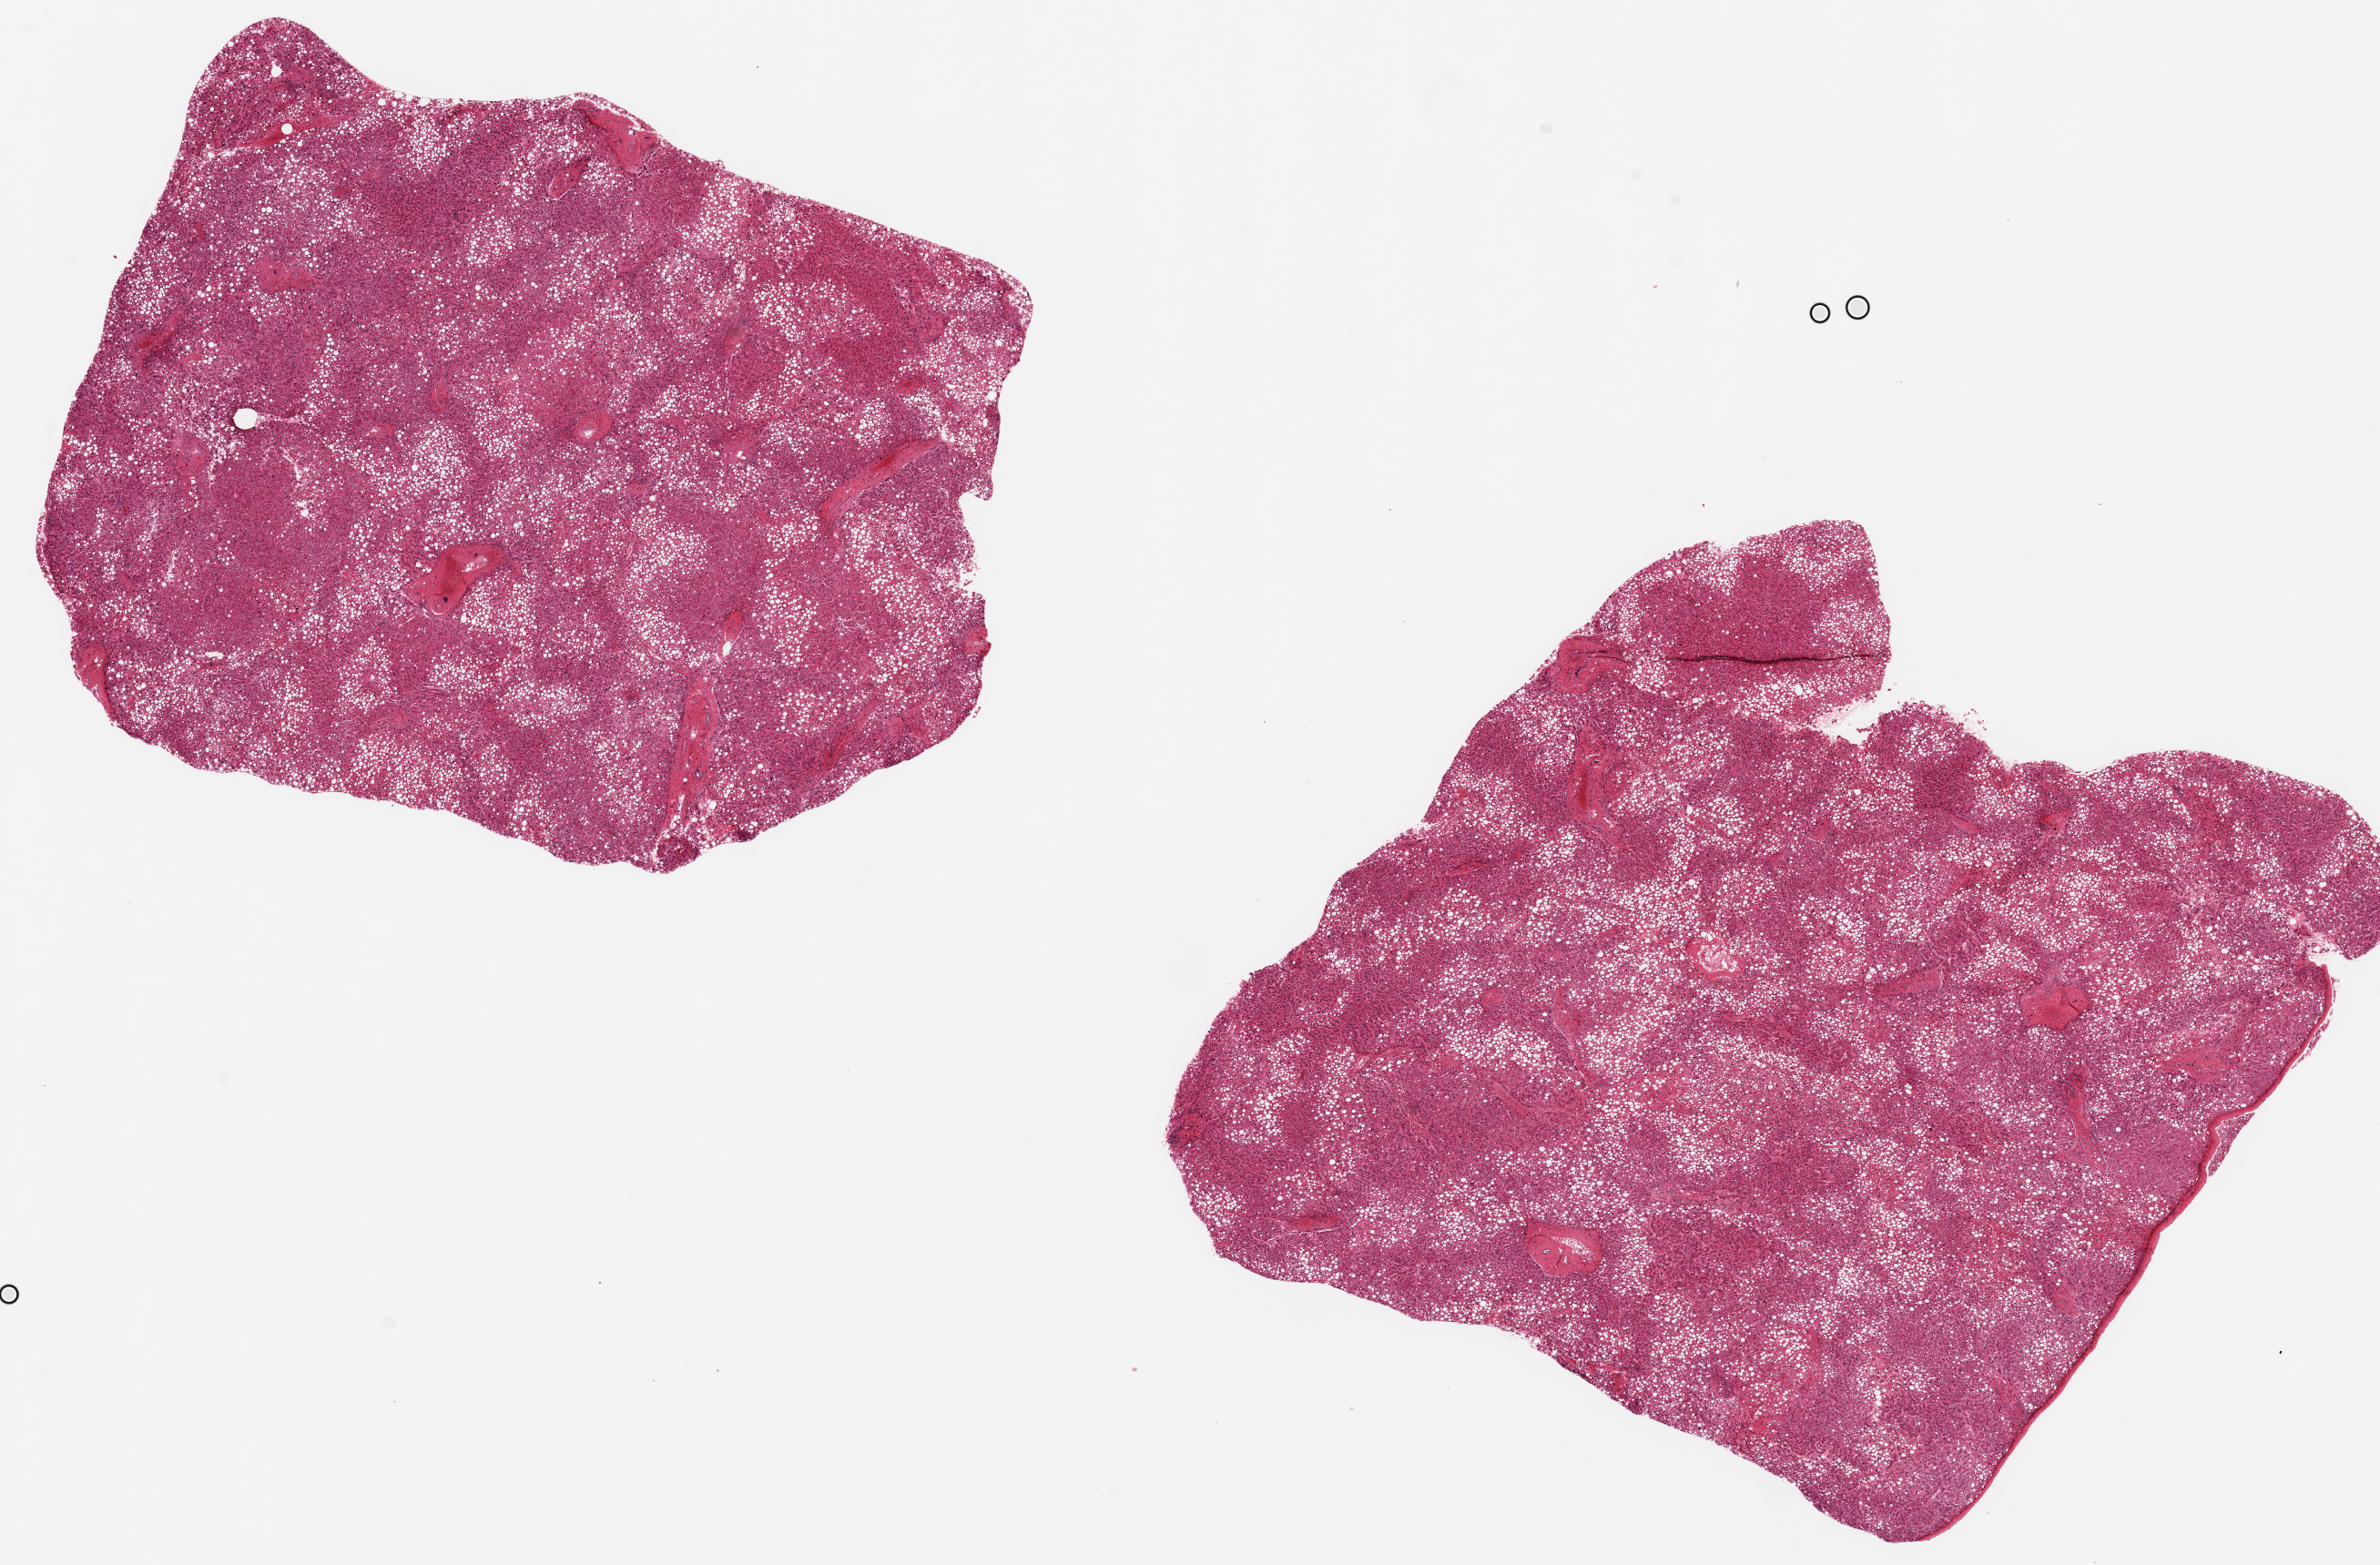
Whole-slide image, haematoxylin and eosin stain, brightfield, low-resolution overview of the scanned area, about 20.7 x 13.6 mm, PAXgene-fixed paraffin-embedded (PFPE) section, target tissue: liver, tissue donor sample. Male donor.
Review note (as recorded): 2 pieces, 7x7 & 8x8mm; 60% macrovesicular steatosis.